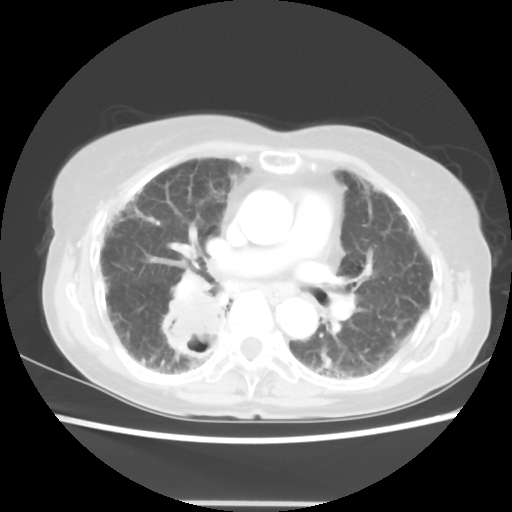
Chest CT, one axial slice; position 29 of 52 along the scan axis; reconstruction kernel STANDARD; lung window (W 1500 / L -600 HU); 5 mm slice thickness; 512 × 512 image matrix, field of view 325 × 325 mm. Patient: female, 71 years. Case-level facts recorded for this patient, not image findings: clinical TNM (as recorded): T3 N0 M0.
Annotated regions visible in this slice (rectangle marked by the reading radiologist):
- lung tumour (recorded histology: squamous cell carcinoma): bounding box <156,290,231,368> (left, top, right, bottom; pixels)